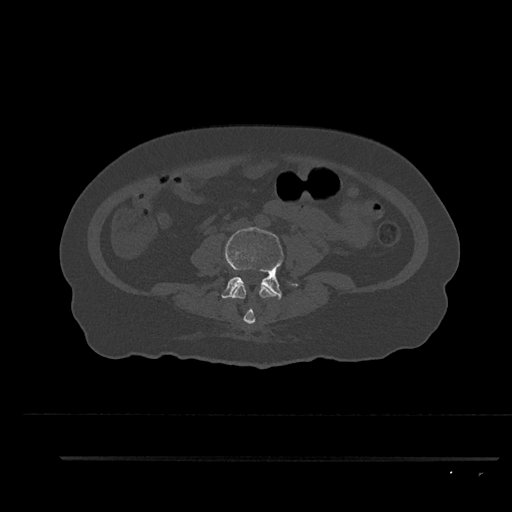
CT including the spine, one axial slice. Slice 44 of 797 in the series (ordered by position). 120 kVp. Bone window (W 1800 / L 400 HU). 512 × 512 image matrix, field of view 408 × 408 mm. Patient: female, 44 years. From the clinical record (not read from this slice): primary cancer: renal.
Annotated regions visible in this slice (semi-automatic segmentation, software-assisted and operator-edited):
- L3 vertebra: bounding box (x1, y1, x2, y2) in pixels: (232, 285, 281, 324)
- L4 vertebra: (221, 227, 299, 299)